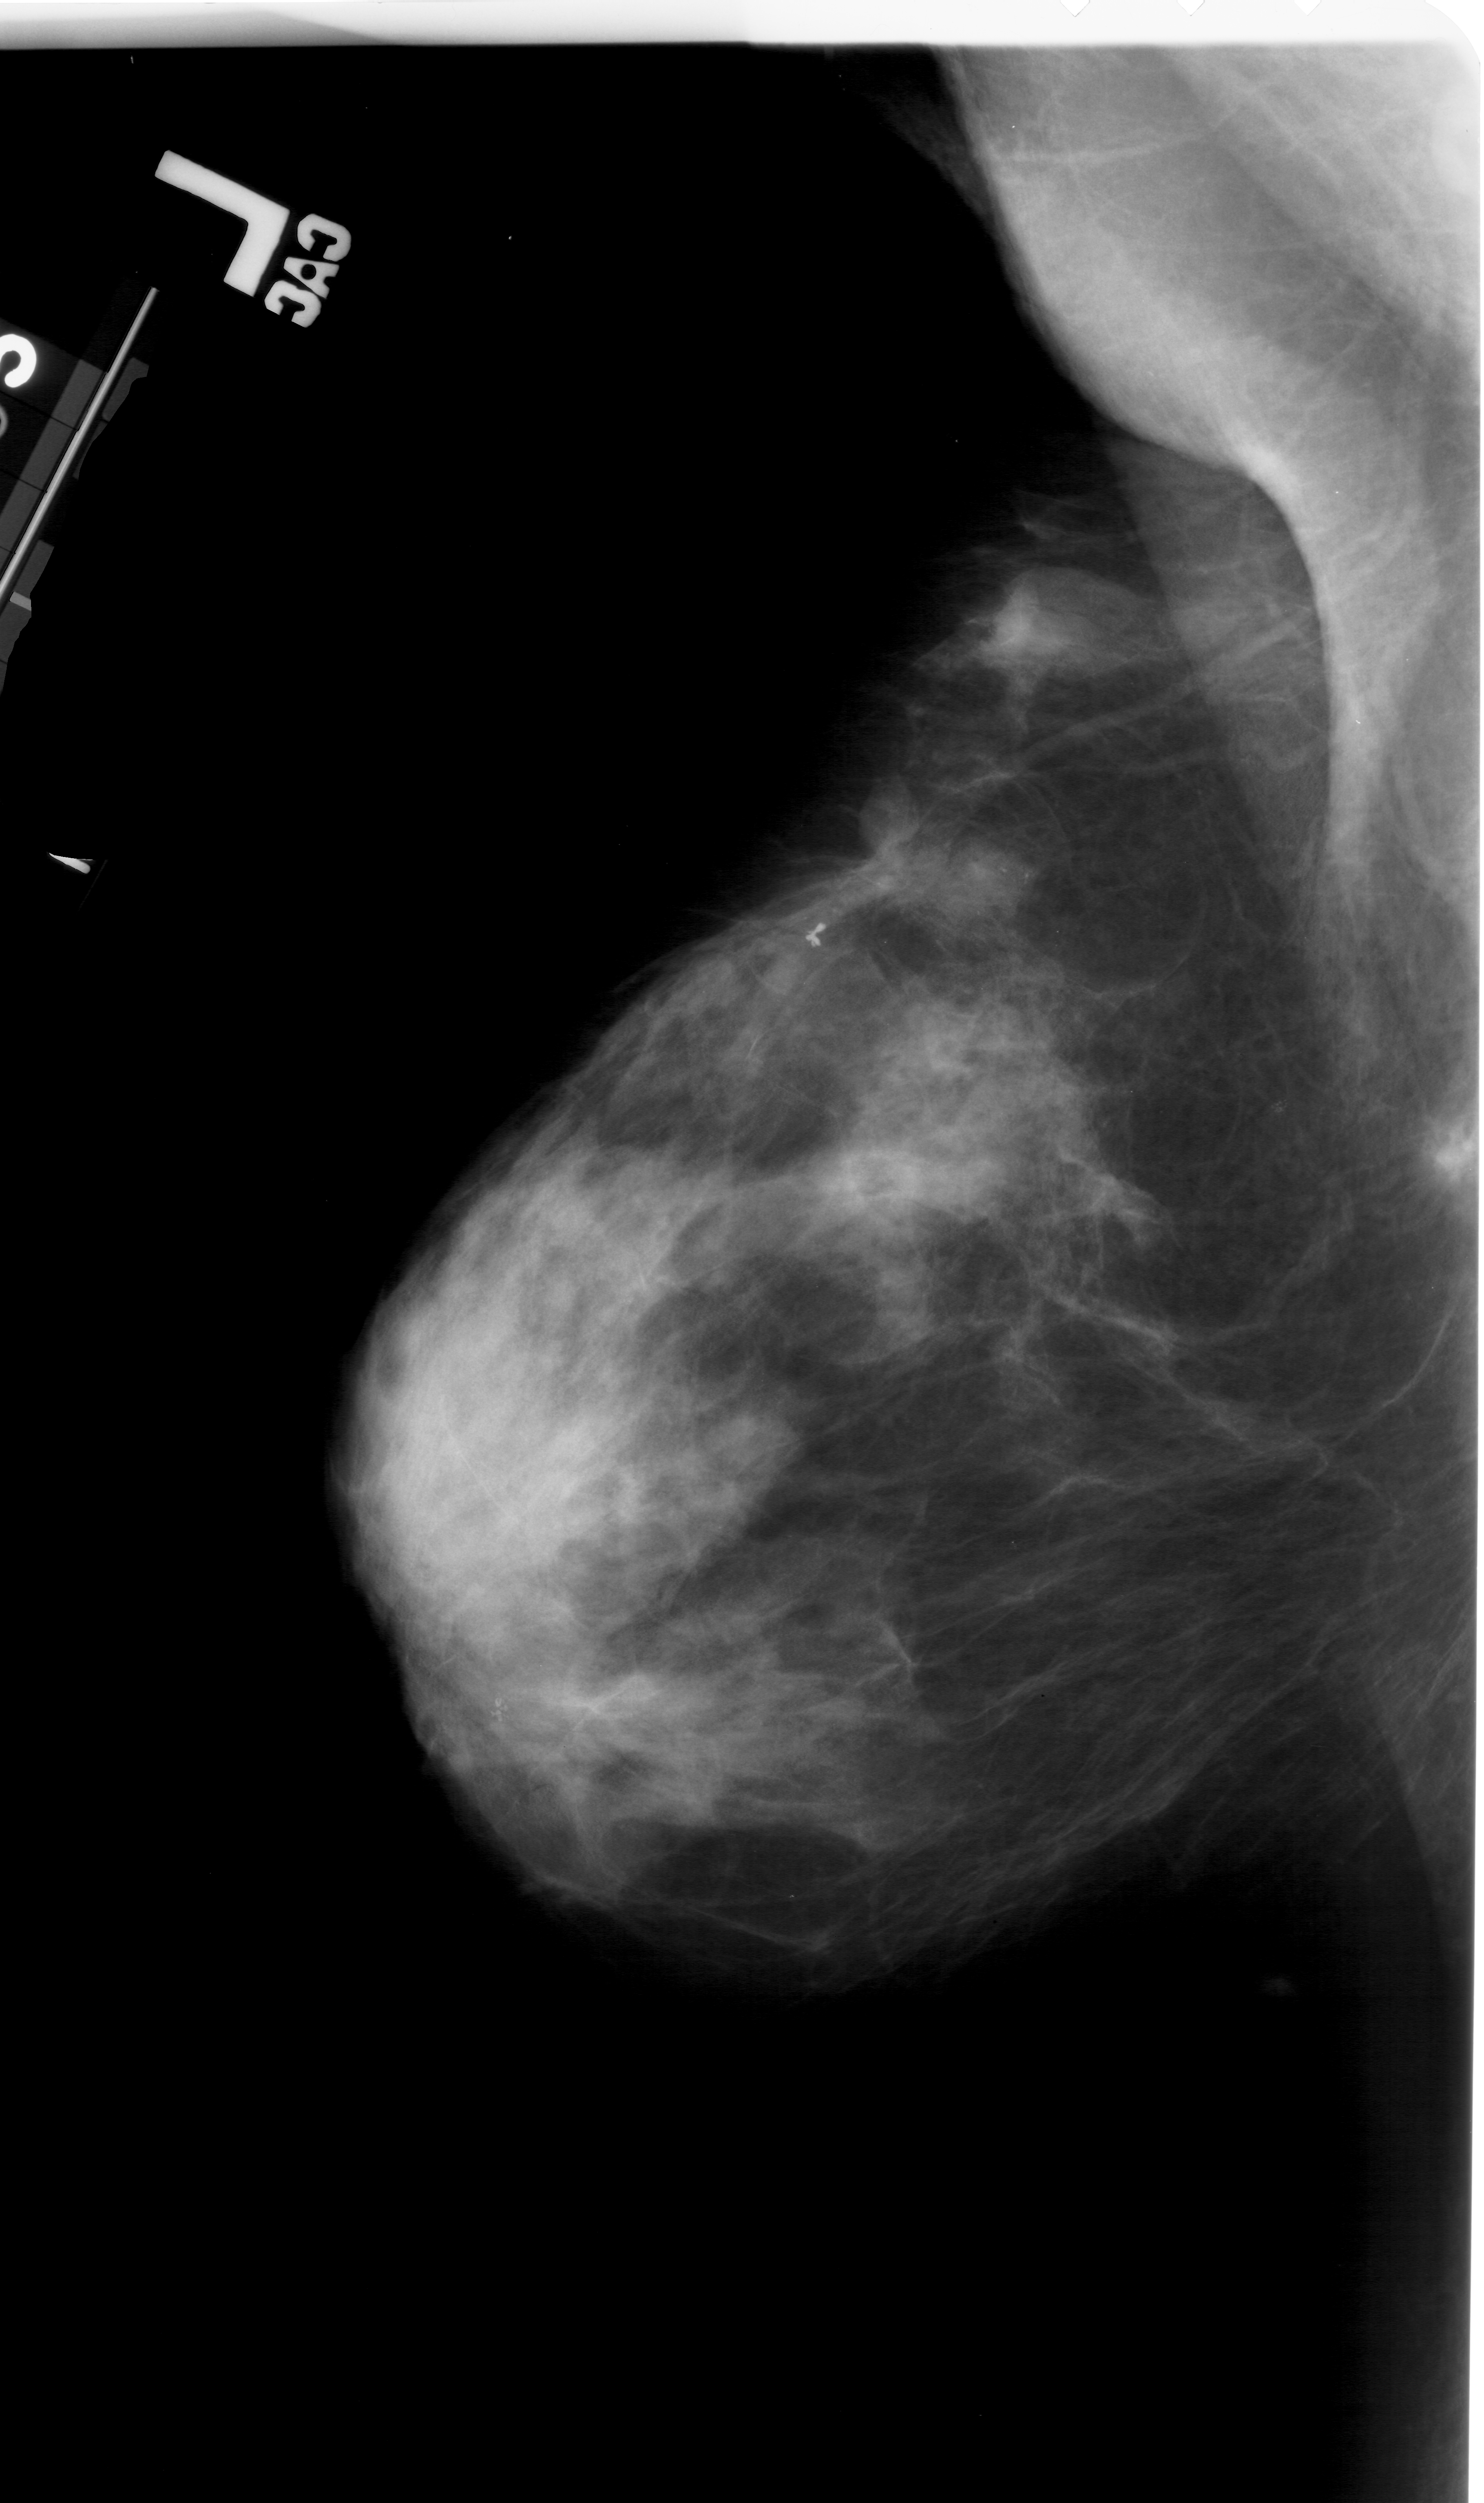
Digitized screen-film mammogram; left breast; MLO view; BI-RADS breast density category 4 (scale 1–4).
- Marked findings (only marked abnormalities are described; nothing is implied about the rest of the image): mass, shape irregular, margins spiculated; BI-RADS assessment category 5; pathology (as recorded): malignant.